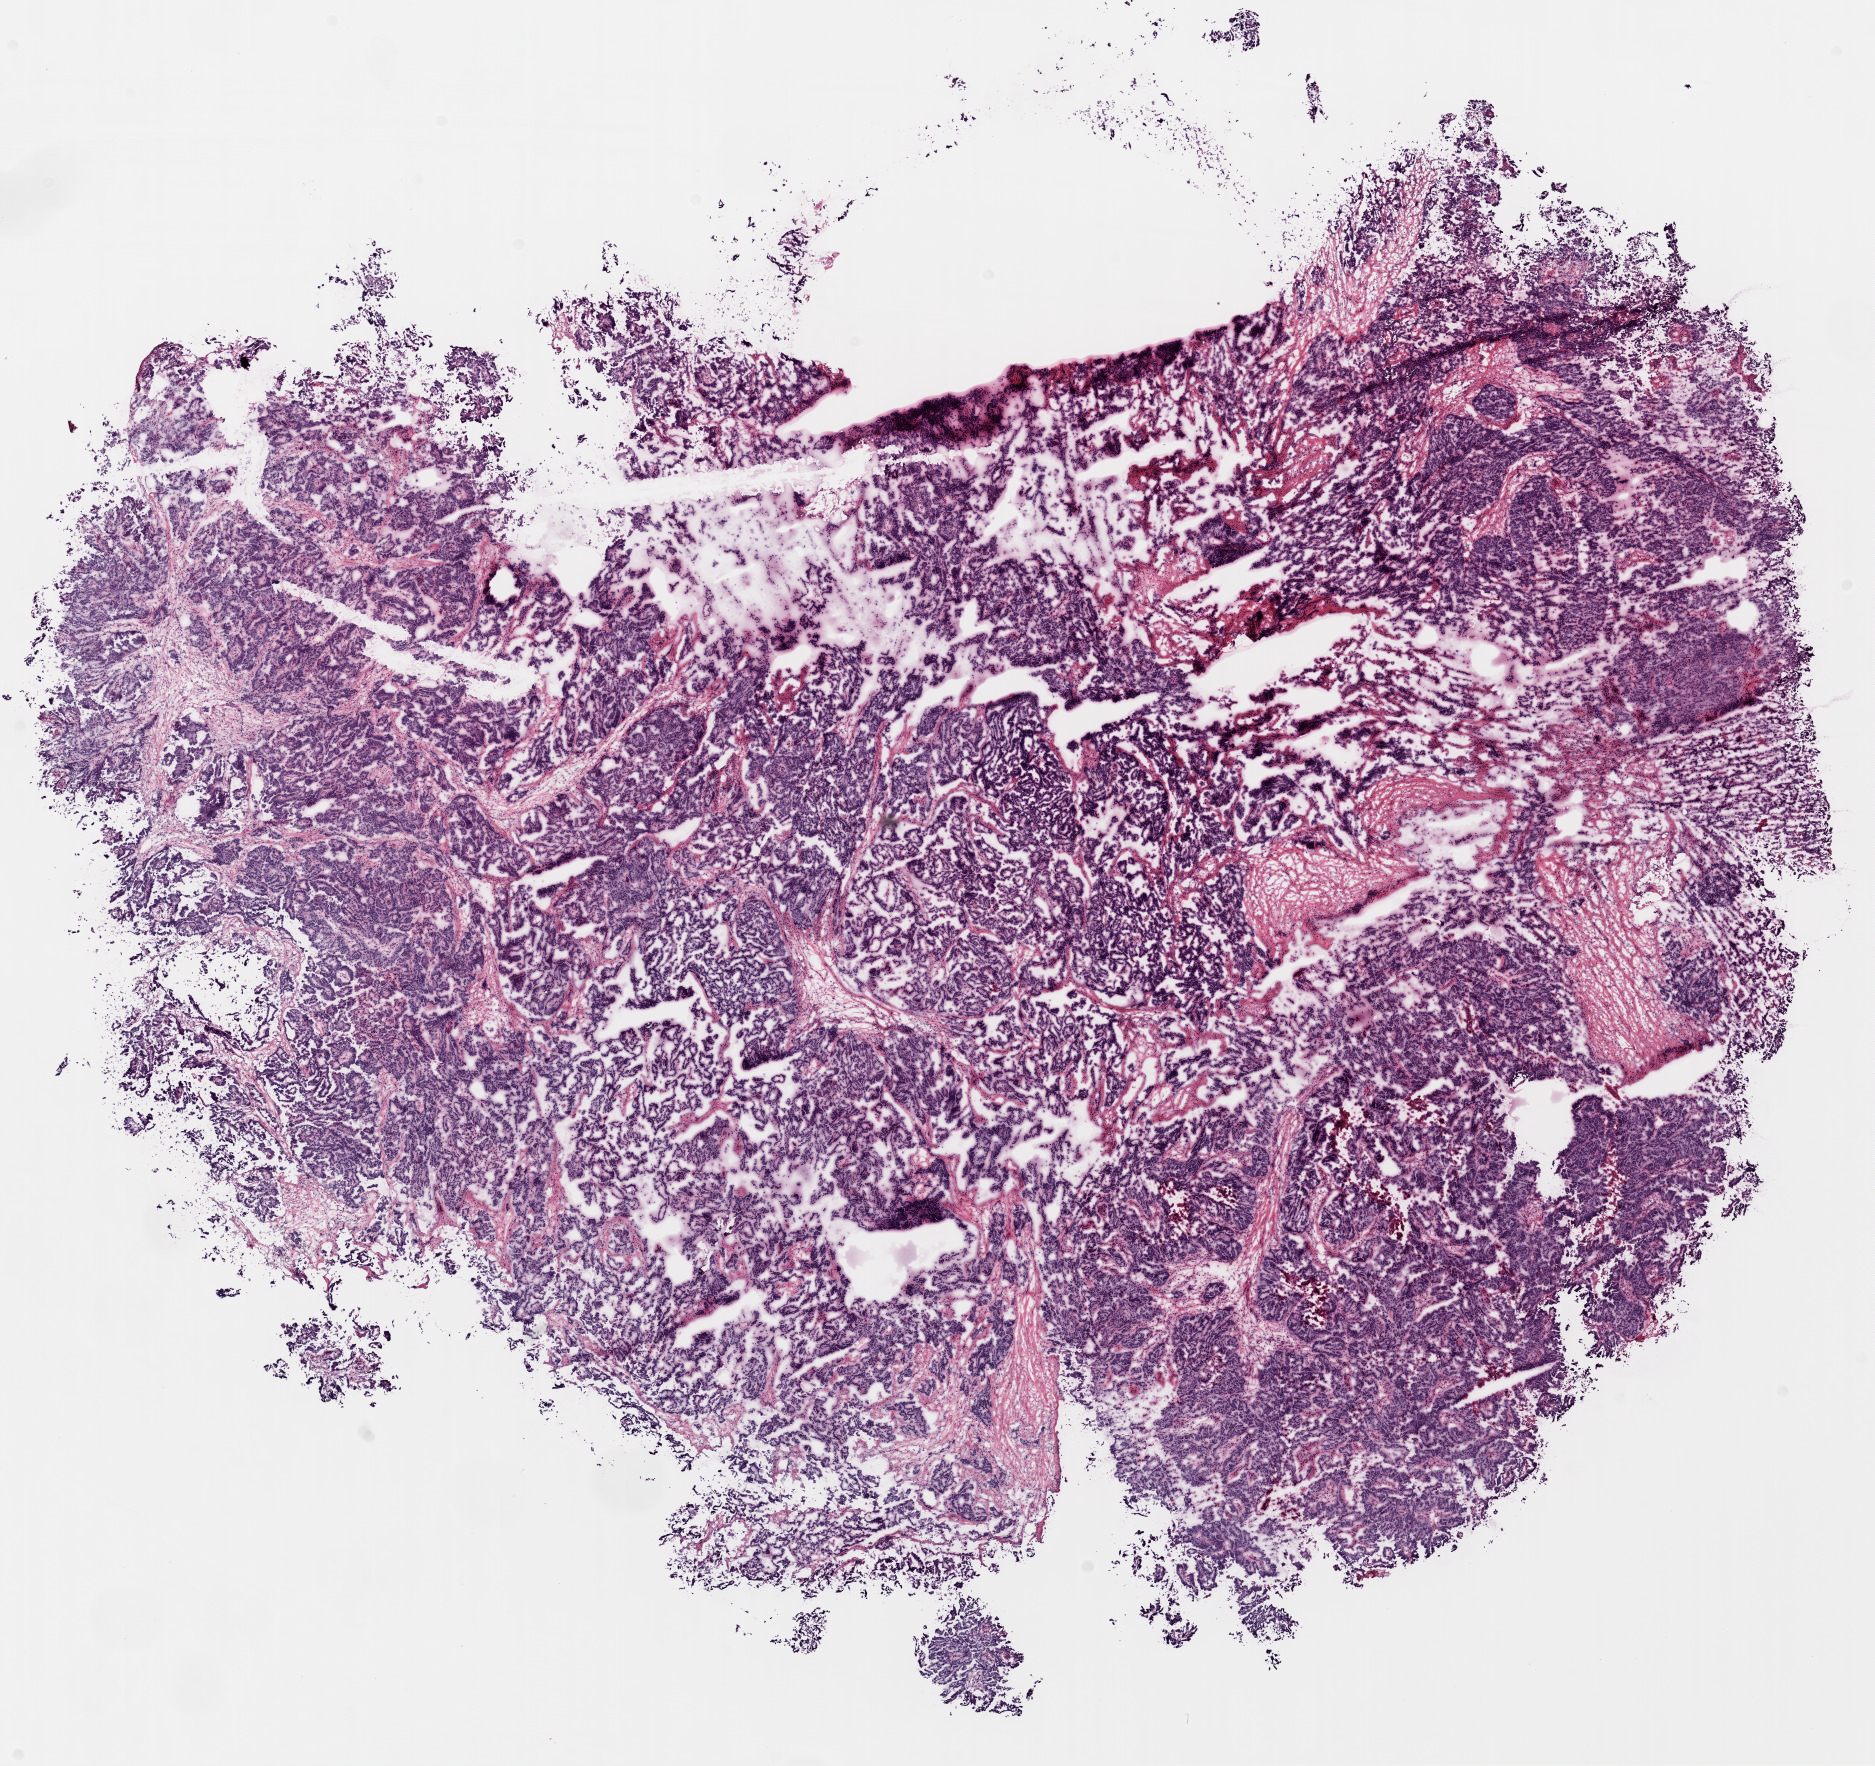
H&E whole-slide image — a low-resolution overview of the entire scanned area, about 15.0 x 14.2 mm (acquisition: 20x scan), frozen section from the top of the tissue portion, primary tumour sample from the ovary. Female patient; age at initial diagnosis 41 years. Histologic grade: G3 (poorly differentiated). Slide review estimates, as recorded: tumour cells 89%, tumour nuclei 90%, normal cells 0%, stromal cells 10%, necrosis 1%.
Histologic diagnosis: Serous cystadenocarcinoma, NOS. FIGO stage: IIIC.